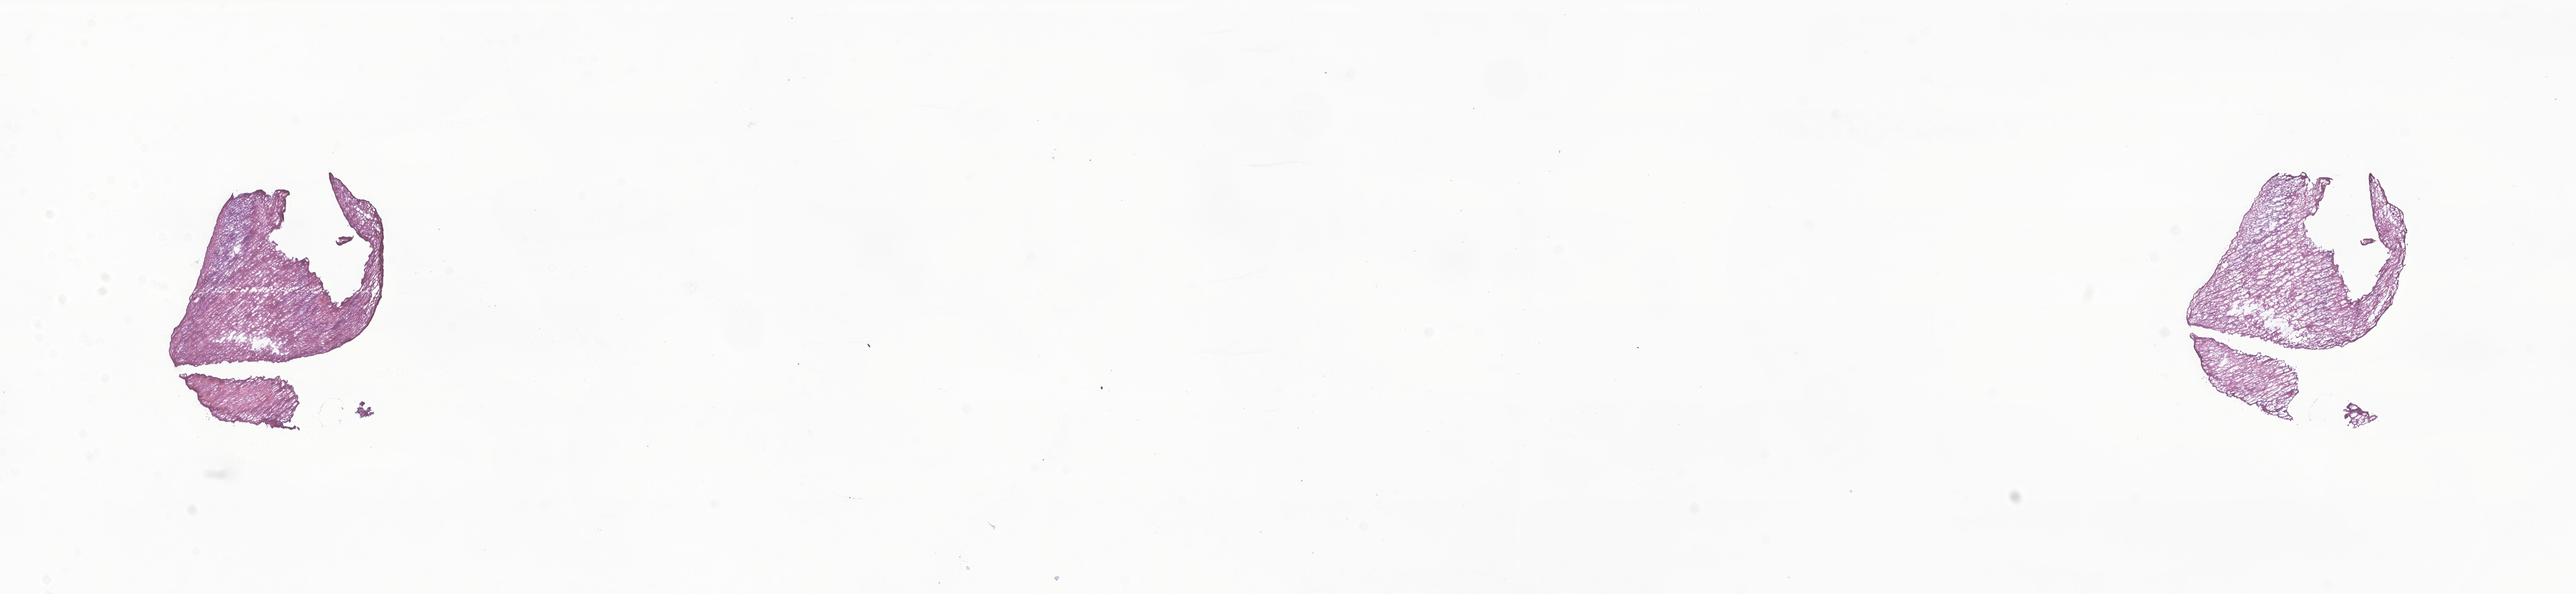
Whole-slide image, hematoxylin and eosin (H&E) stain of tumor tissue from the brain — shown as a low-resolution overview of the whole scanned area (about 28.2 x 6.5 mm). Frozen section. Male patient, age 96 months (8 years).
Diagnosis: Pilocytic astrocytoma.